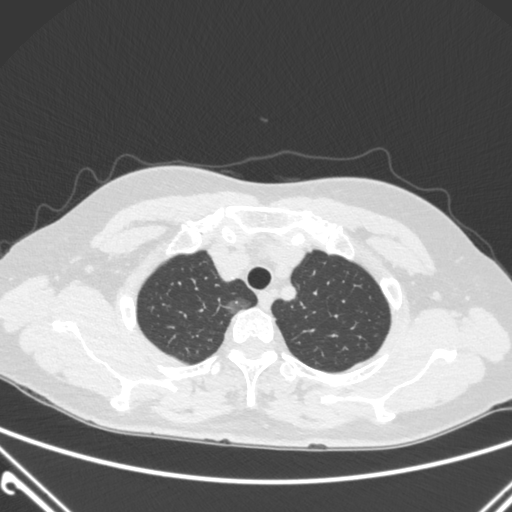
Chest CT, one axial slice; slice 242 of 300 in the series (ordered by position); lung window (W 1500 / L -600 HU); 512 × 512 image matrix, field of view 350 × 350 mm. Patient: female, 54 years. From the clinical record (not read from this slice): clinical TNM (as recorded): T1a N0 M0.
Annotated regions visible in this slice (bounding box drawn by a radiologist):
- lung tumour (recorded histology: adenocarcinoma): bounding box [x1, y1, x2, y2] px = [222, 292, 254, 319]